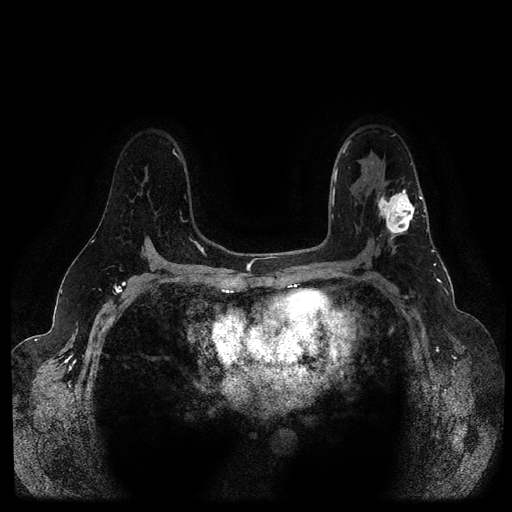
Breast MRI (dynamic contrast-enhanced, multi-phase), one axial slice. Position 69 of 116 along the scan axis. Dynamic contrast-enhanced series, time point 2 of 5 at this slice position (early post-contrast). 1.5 T. TE 2.6 ms, TR 5.3 ms. 2 mm slice thickness. 512 × 512 image matrix. Patient: female, 54 years.
Structures marked on this image (semi-automatically segmented with operator editing):
- breast lesion (labelled 'tumour' in the annotation; benign lesions carry a separate 'benign' label): bounding box <376,188,419,243> (left, top, right, bottom; pixels)